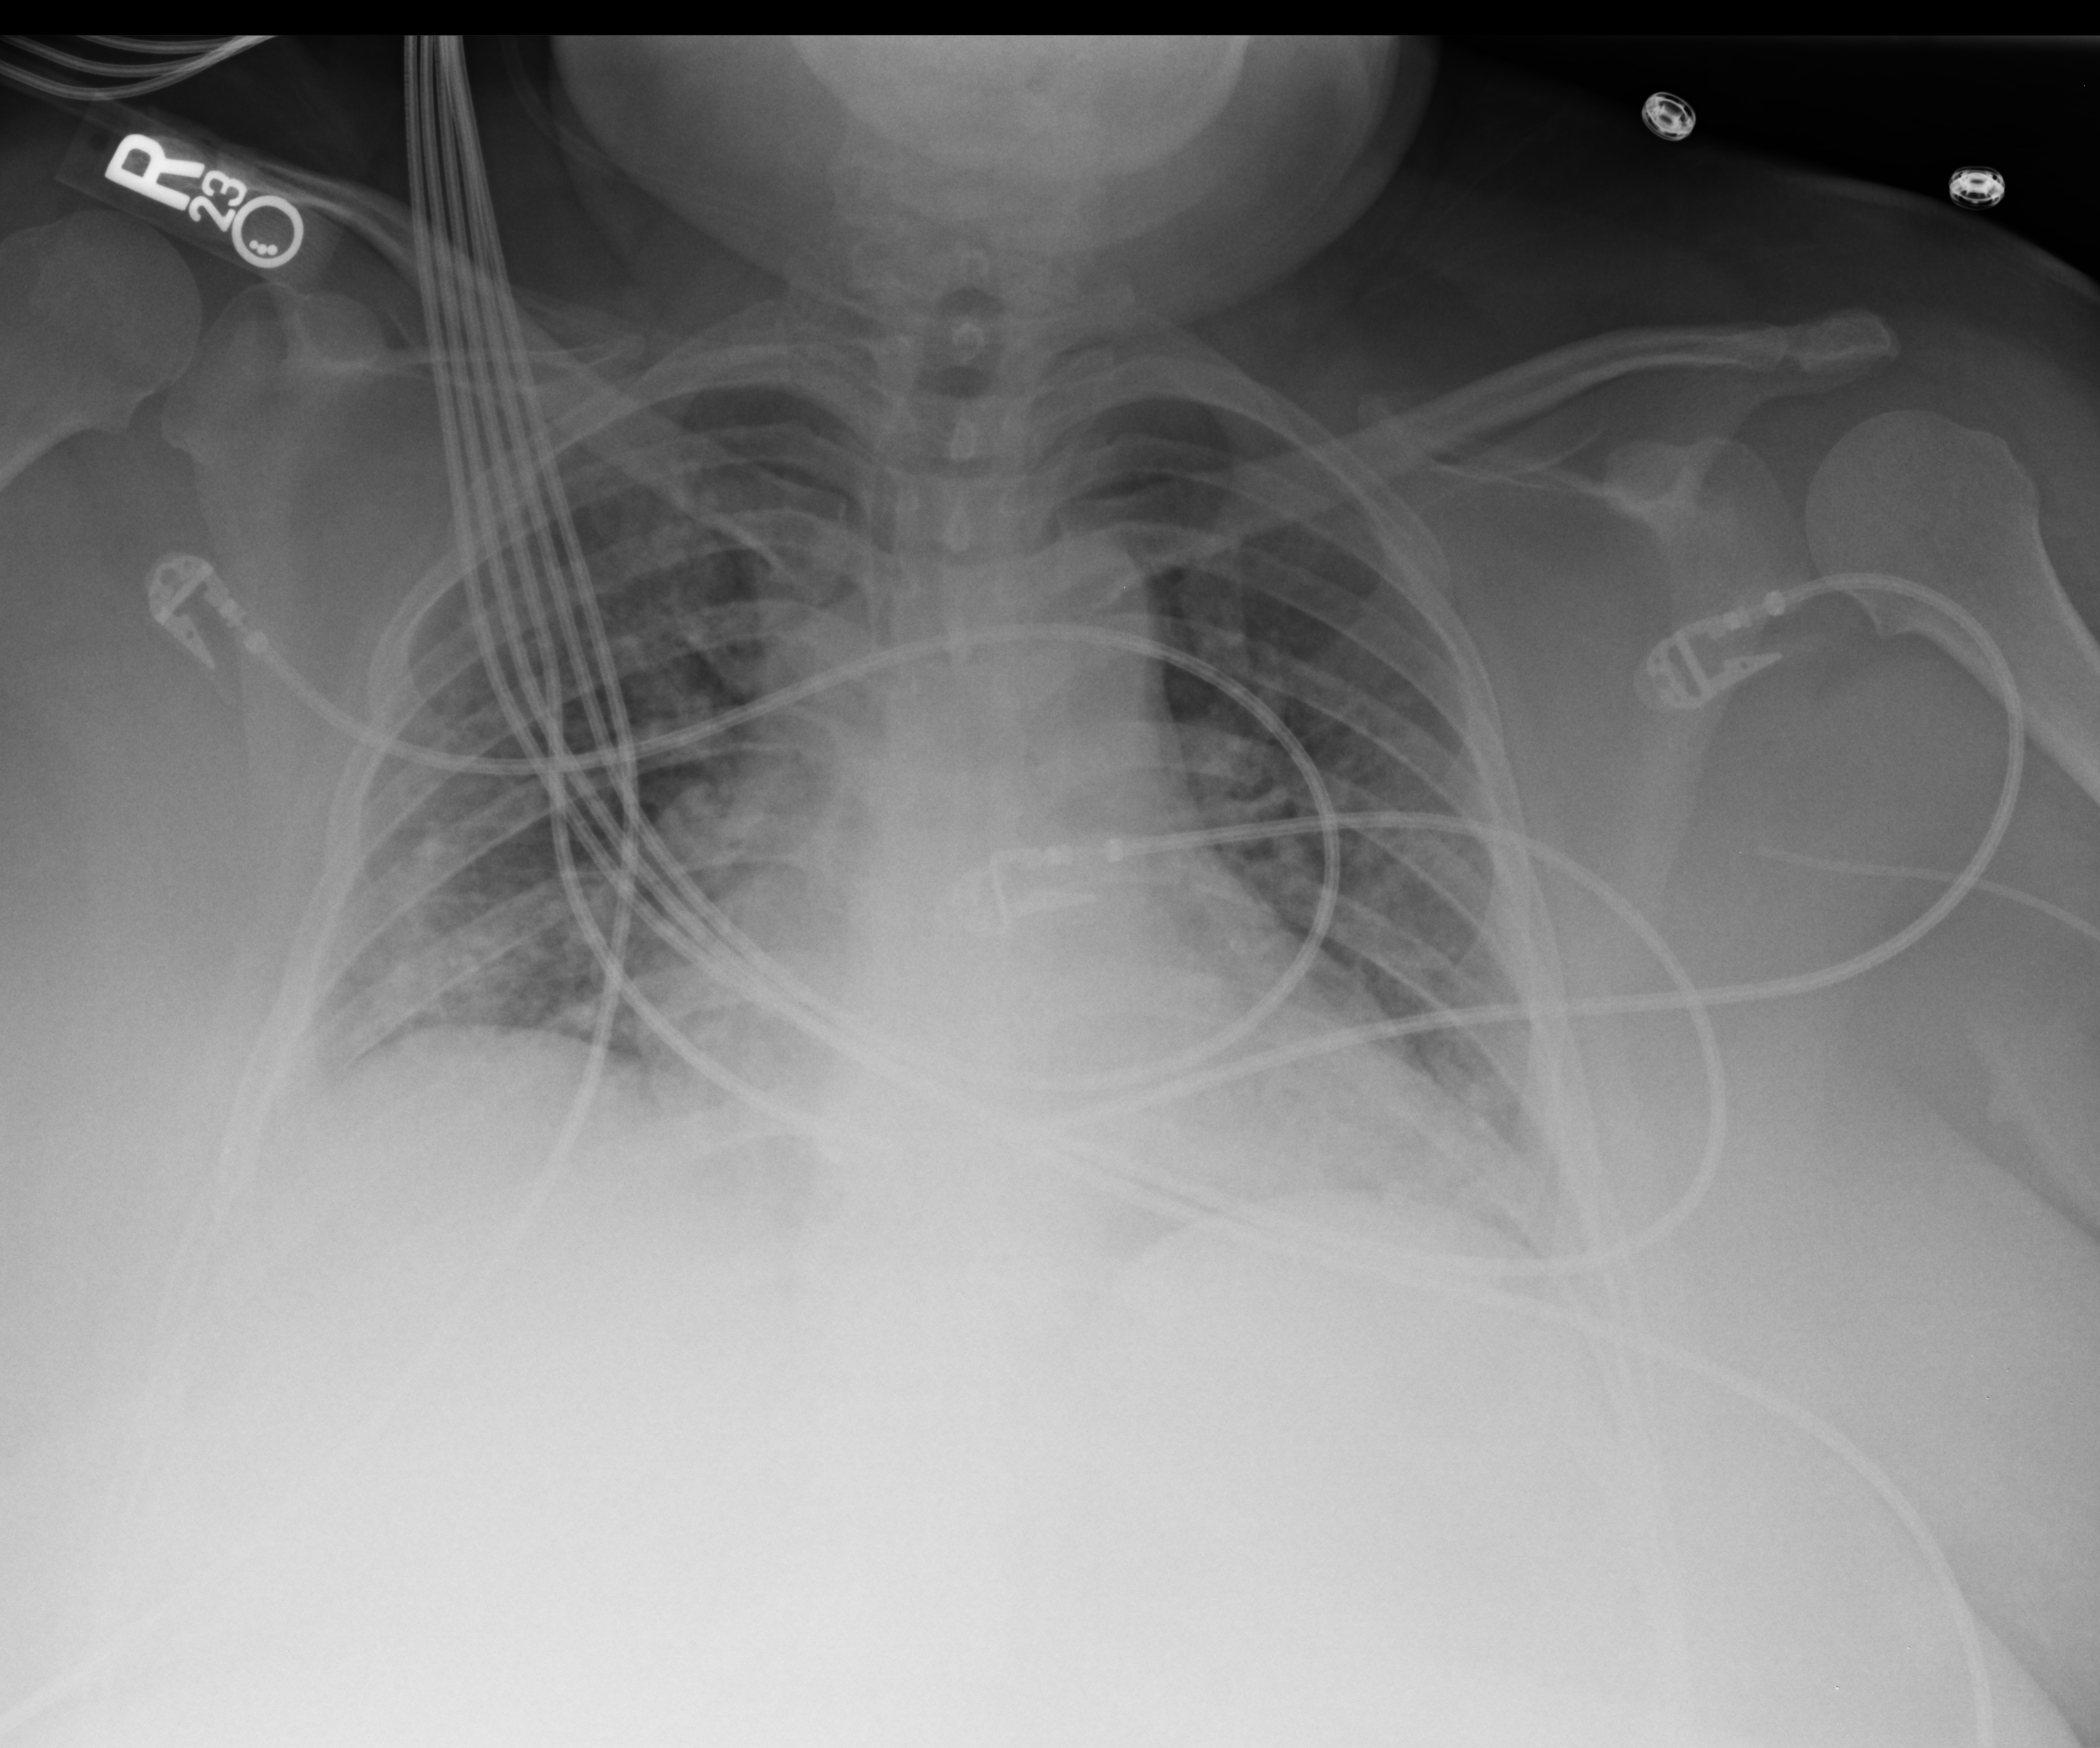
Bedside chest radiograph (computed radiography); anteroposterior (AP) projection. Female patient hospitalised with COVID-19, age 18–59 years.
Admission-level facts for this patient (not findings on this image; timing relative to this image not recorded):
- admitted to intensive care during this hospital stay: yes